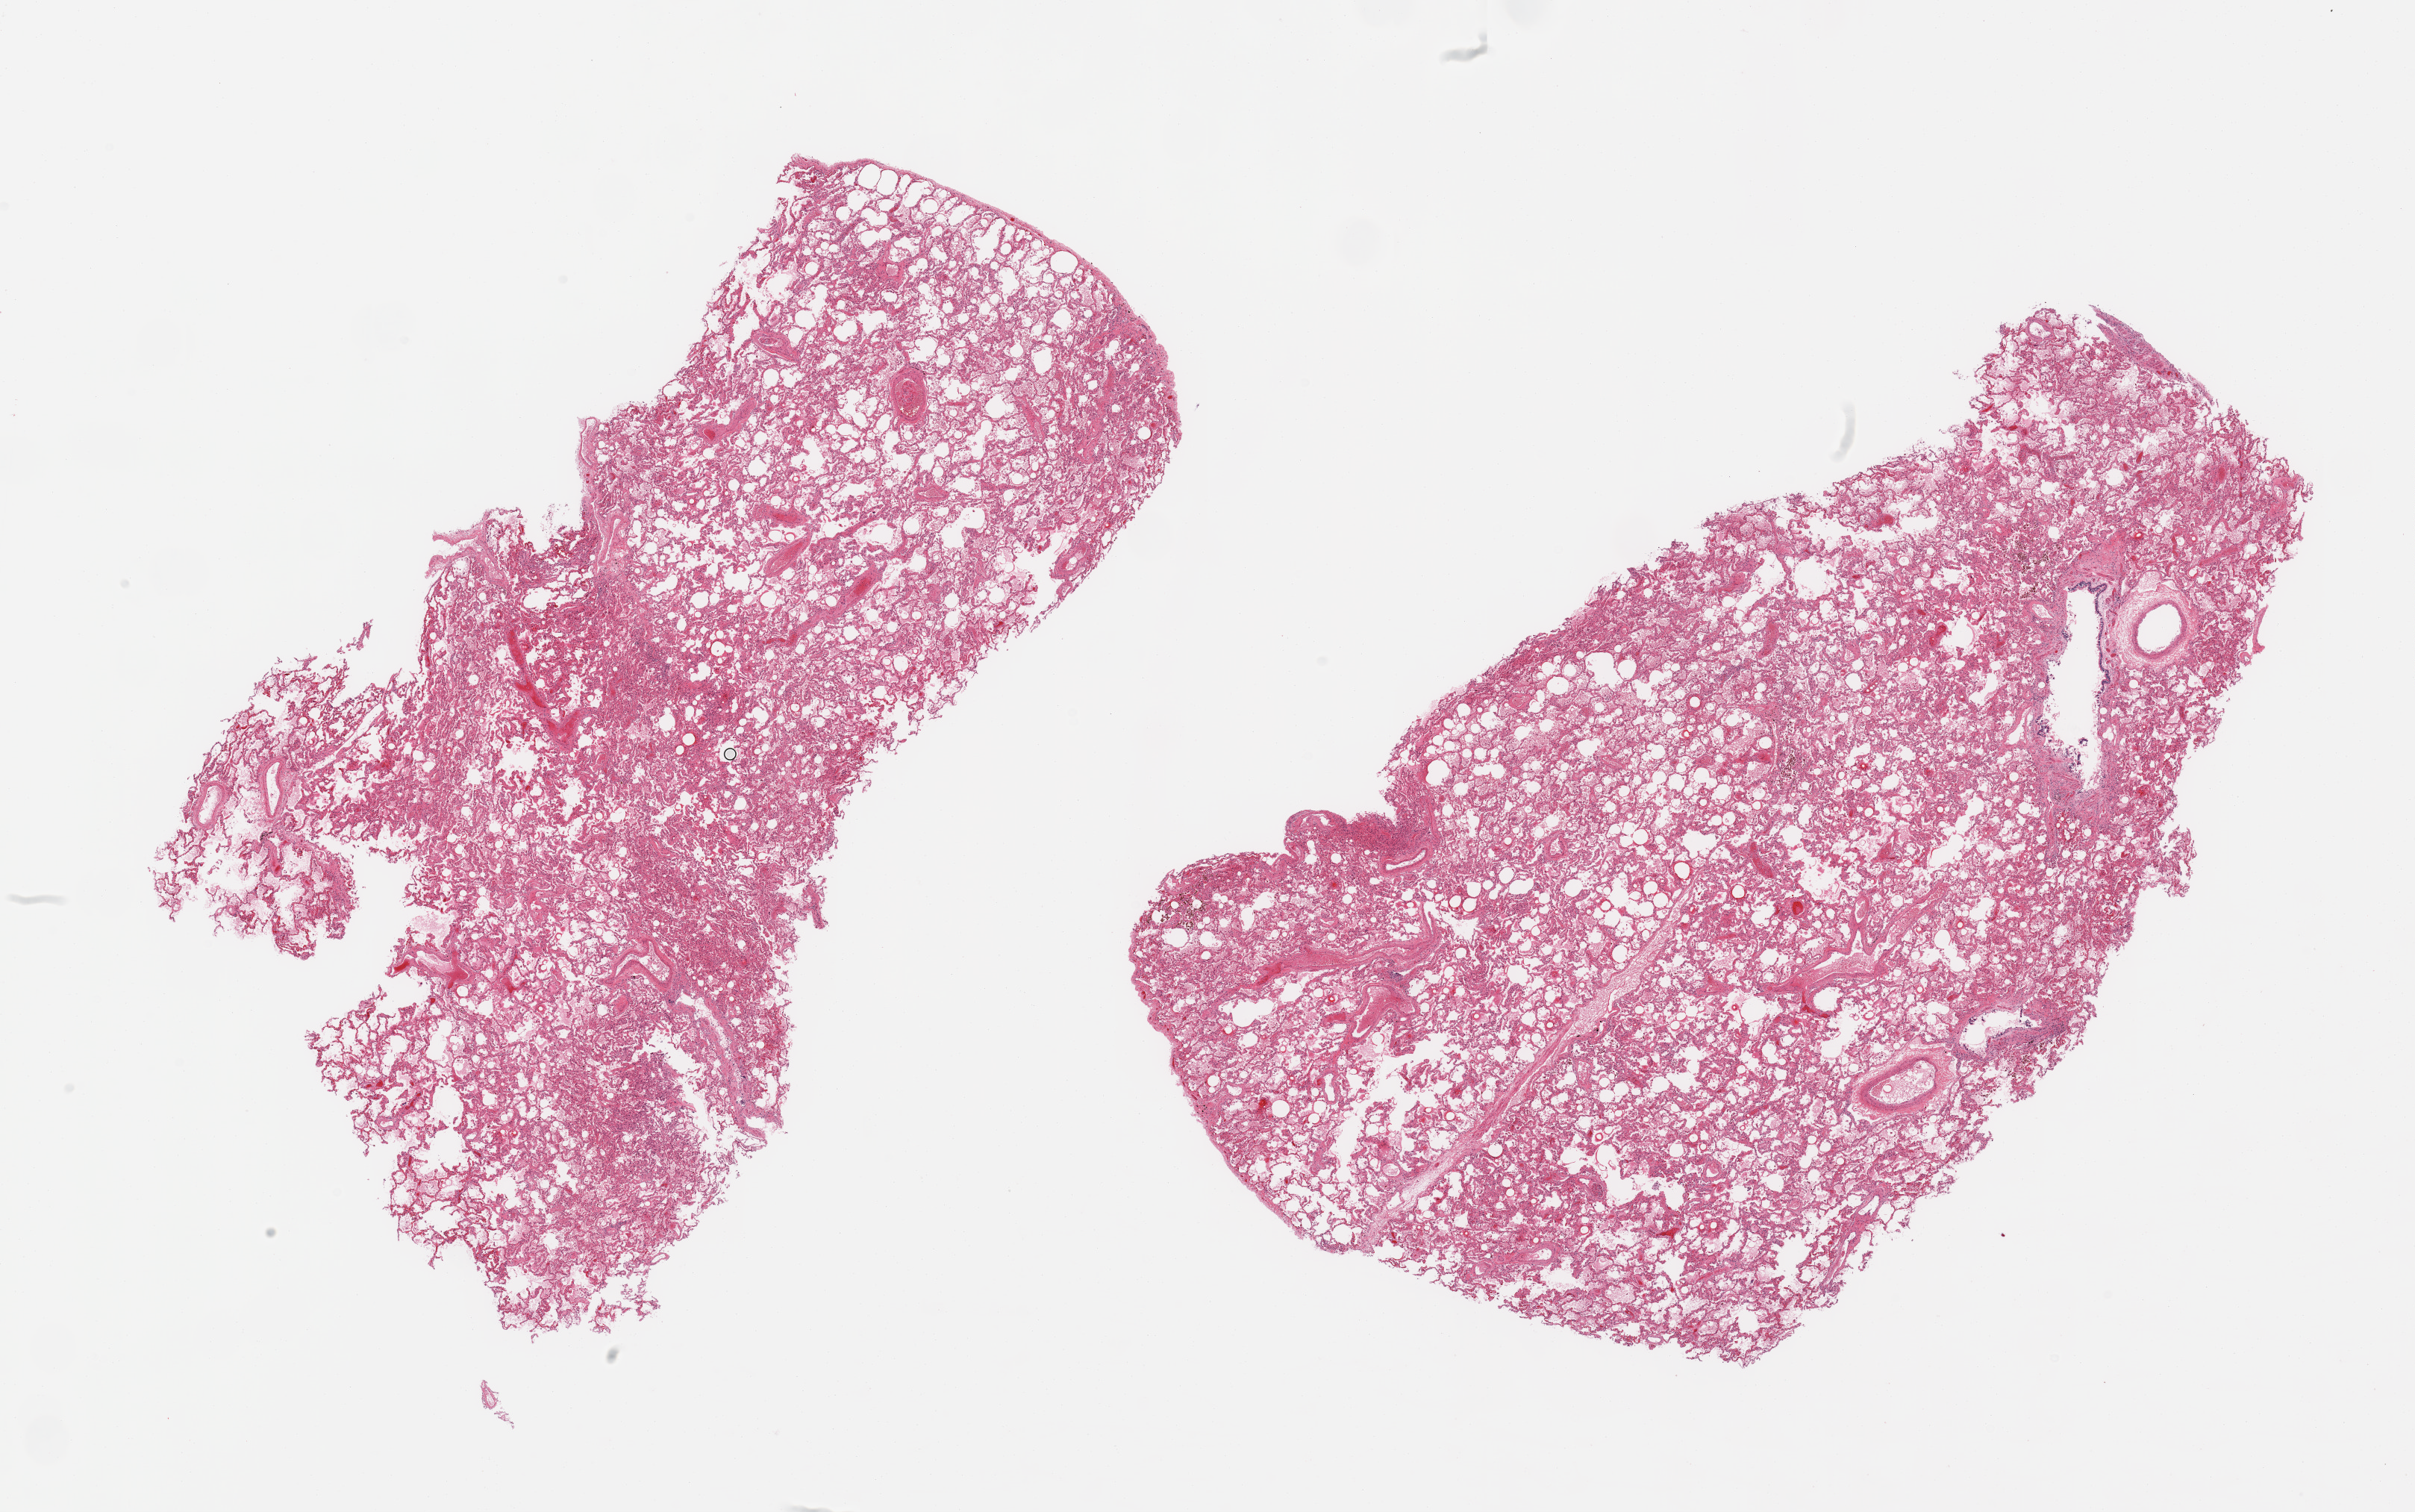
H&E whole-slide image, brightfield — whole scanned area (about 25.6 x 16.0 mm) shown as a low-resolution overview, PAXgene-fixed paraffin-embedded (PFPE) section, target tissue: lung, donor tissue sample. Male donor.
- pathologist's review note for this sample: 2 pieces; slight pulmonary edema; scattered alveolar macrophages